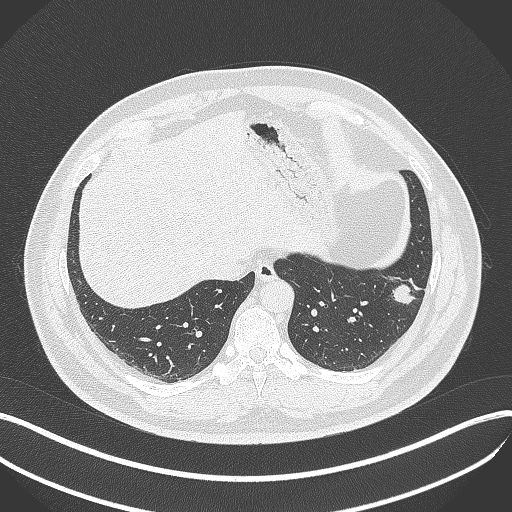
Chest CT, one axial slice; reconstruction kernel B70f; lung window (W 1500 / L -600 HU); 1 mm slice thickness; 512 × 512 image matrix, field of view 400 × 400 mm. Patient: male, 39 years. Case-level facts recorded for this patient, not image findings: clinical TNM (as recorded): T2a N0 M0; histopathological grade: G2-3.
Structures marked on this image (rectangle marked by the reading radiologist):
- lung tumour (recorded histology: adenocarcinoma): bounding box [x1, y1, x2, y2] px = [390, 278, 418, 308]